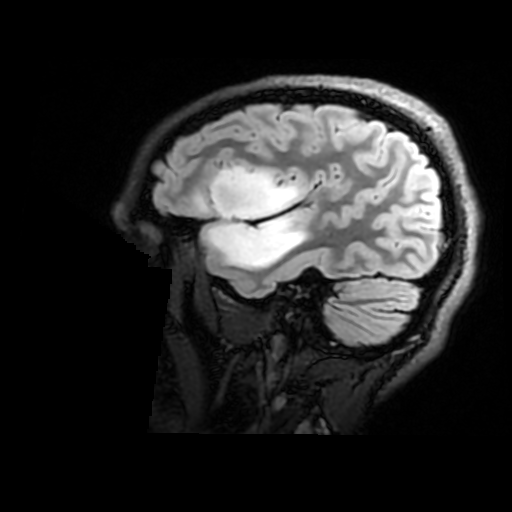
Brain MRI from a brain-tumour surgery series, one sagittal slice. Position 132 of 176 along the scan axis. T2 FLAIR. 1 mm slice thickness. 512 × 512 image matrix. From the clinical record (not read from this slice): histopathology: Astrocytoma; WHO grade: 2; IDH mutation: yes; tumour location: Right Insular.
Annotated regions visible in this slice (manually delineated by an expert):
- tumour: bounding box [x1, y1, x2, y2] px = [209, 166, 307, 270]